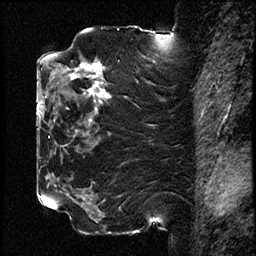
Breast MRI (dynamic contrast-enhanced), one sagittal slice. Position 44 of 78 along the scan axis. Dynamic contrast-enhanced study with each time point stored as its own series, time point 2 of 3 at this slice position (early post-contrast, ordered by acquisition time). 1.5 T. TE 4.2 ms, TR 17.6 ms. 2 mm slice thickness. 256 × 256 image matrix, field of view 200 × 200 mm. Female patient, age 42 years. Case-level facts recorded for this patient, not image findings: setting: breast cancer imaged before/during neoadjuvant chemotherapy; receptor status: HER2-positive.
Structures marked on this image (semi-automatically segmented with operator editing):
- analysis volume of interest (the breast-tissue region the enhancement analysis was run in; not a lesion): bounding box [x1, y1, x2, y2] px = [50, 48, 109, 129]
- tumour enhancement mask (voxels above the 100 % enhancement threshold inside the analysis volume of interest): [71, 63, 108, 96]